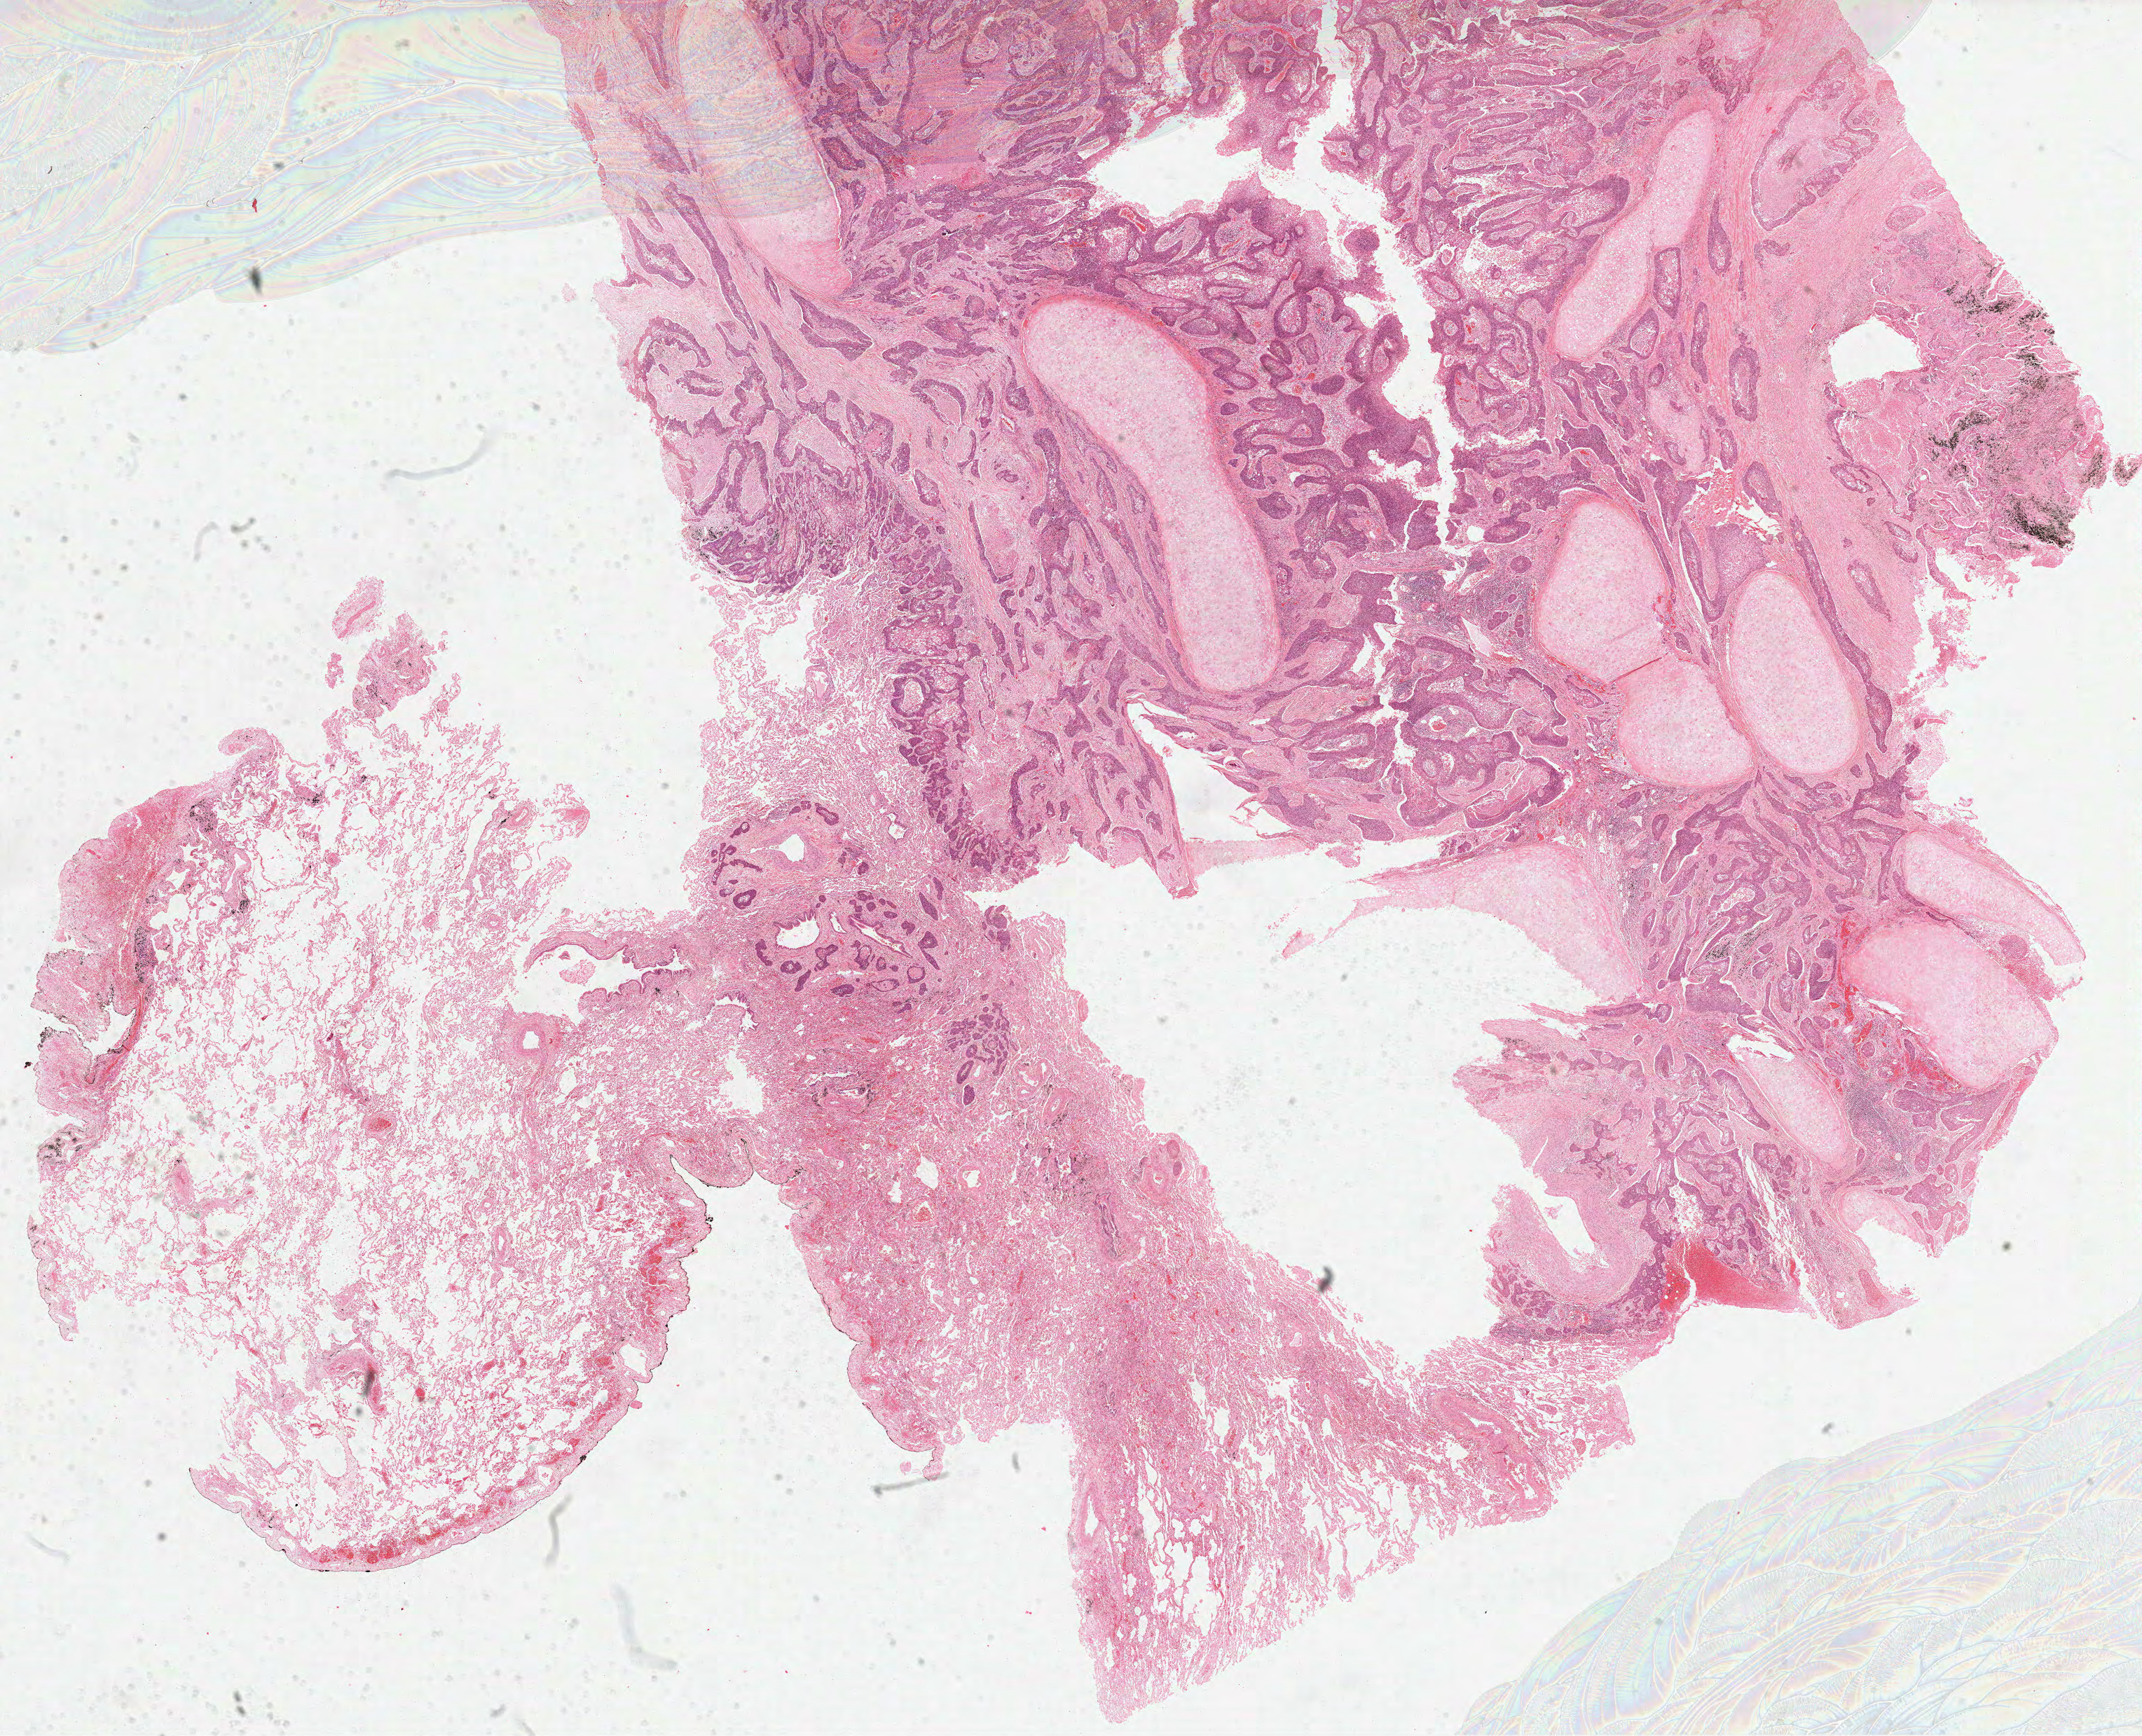
H&E whole-slide image, low-resolution overview of the scanned area, about 24.7 x 20.0 mm, FFPE section, lung, primary tumour sample. Patient: male, age at initial diagnosis 60 years.
Diagnosis: Squamous cell carcinoma, NOS. AJCC pathologic stage: IIIA (6th edition). Laterality: left.